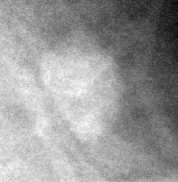
Cropped region of a digitized screen-film mammogram centred on a radiologist-marked abnormality, left breast, MLO view.
Finding: mass, shape lymph node, margins circumscribed; BI-RADS assessment category 2; subtlety rating 4 on a 1 (subtle) to 5 (obvious) scale; benign without callback (not worked up further).